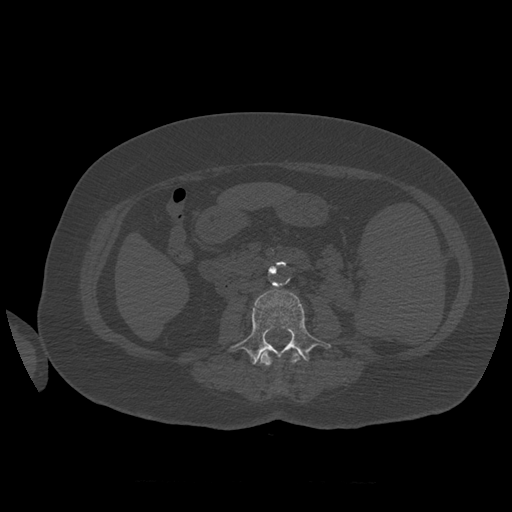
CT including the spine, one axial slice. Slice 234 of 399 in the series (ordered by position). Reconstruction kernel STANDARD. Bone window (W 1800 / L 400 HU). 512 × 512 image matrix, field of view 404 × 404 mm. Patient age 81 years. From the clinical record (not read from this slice): primary cancer: renal; vertebrae with lytic lesions (as recorded): L1.
Structures marked on this image (semi-automatic segmentation, software-assisted and operator-edited):
- L2 vertebra: box from (x=253, y=351) to (x=301, y=383) px
- L3 vertebra: (x=228, y=289)–(x=331, y=364)